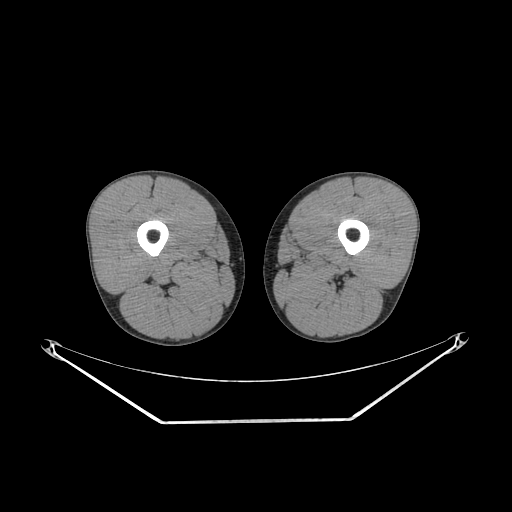
CT of an extremity soft-tissue mass (from a PET/CT study), one axial slice. Slice 216 of 267 in the series (ordered by position). 140 kVp. Soft-tissue window (W 400 / L 40 HU). 3.75 mm slice thickness. 512 × 512 image matrix, field of view 500 × 500 mm. Male patient. From the clinical record (not read from this slice): histological type: extraskeletal osteosarcoma; grade: high; site of the primary tumour: left adductur.
Annotated regions visible in this slice (expert contour drawn on MRI and transferred to this co-registered scan by the dataset authors):
- gross tumour volume (mass): bounding box [x1, y1, x2, y2] px = [288, 253, 352, 277]